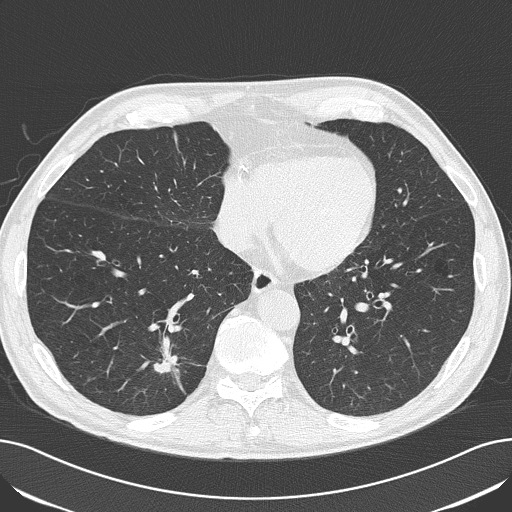
Chest CT (low-dose screening protocol), one axial image. Baseline annual screen. Lung window (W 1500 / L -600 HU). 2 mm slice thickness. Lung (sharp) reconstruction kernel (B50f). 512 × 512 image matrix. Male, age 71 years at enrolment.
- Expert reader's lesion annotation, box from (x=135, y=330) to (x=197, y=392) px.
- The exam's reader record, not a measurement of the box and not confirmed to be the same lesion: non-calcified nodule or mass ≥4 mm, right lower lobe, 14 × 14 mm, spiculated (stellate) margins, soft tissue attenuation.
- Official screen result: positive, change unspecified: nodule(s) >= 4 mm or enlarging nodule(s), mass(es), or other non-specific abnormalities suspicious for lung cancer.
- Later outcome: lung cancer diagnosed 145 days after this screen — adenocarcinoma, NOS, right lower lobe, moderately differentiated (G2), stage IA (AJCC 6th edition), 24 mm at pathology.